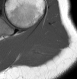
MRI of an extremity soft-tissue mass, one axial slice. Position 19 of 28 along the scan axis. MR volume resampled by the dataset authors to the PET/CT grid (not the native acquisition matrix). 3.27 mm slice thickness. 77 × 79 image matrix. Female patient. Case-level facts recorded for this patient, not image findings: histological type: malignant fibrous histiocytoma; grade: low; site of the primary tumour: left arm.
Annotated regions visible in this slice (expert contour drawn on MRI and transferred to this co-registered scan by the dataset authors):
- gross tumour volume (mass): bounding box [x1, y1, x2, y2] px = [28, 45, 43, 57]